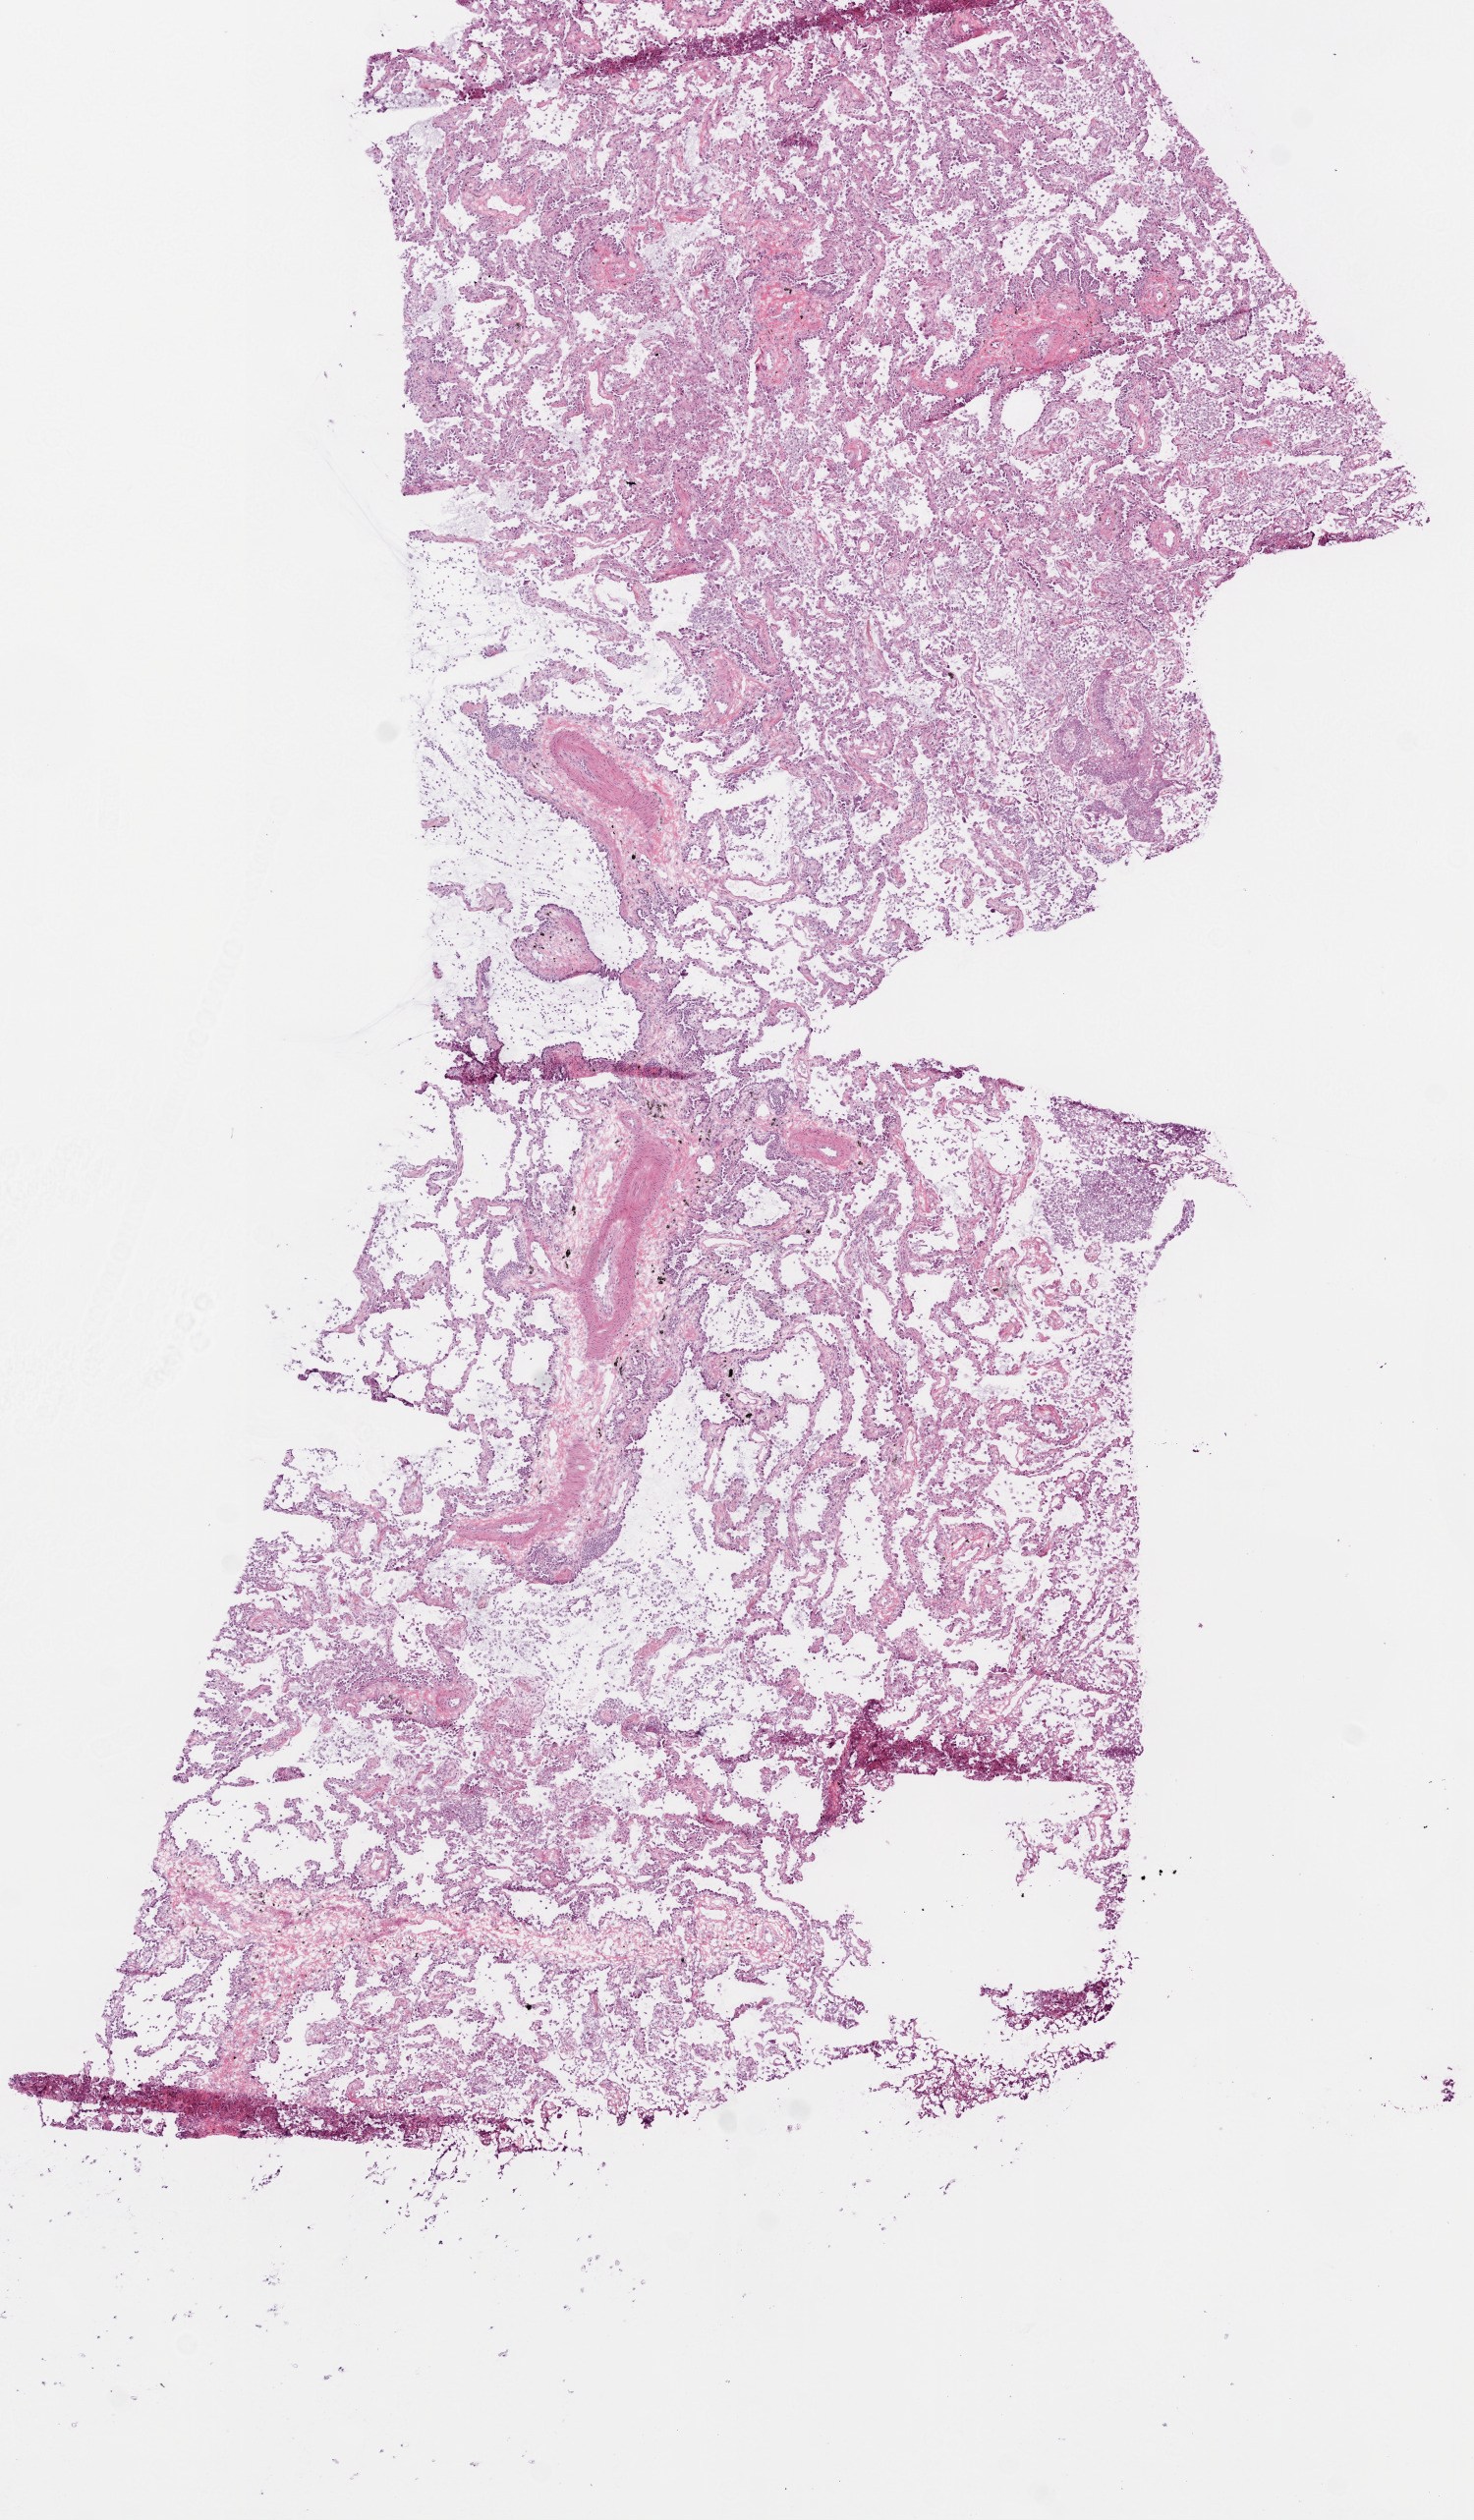
H&E whole-slide image — a low-resolution overview of the entire scanned area, about 6.0 x 10.3 mm (slide scanned at 20x); frozen section from the bottom of the tissue portion; lung, primary tumour sample. Female, age 57 years at initial diagnosis. Composition of this section per pathologist review: tumour cells 95%, tumour nuclei 75%, normal cells 0%, stromal cells 5%, necrosis 0%.
- laterality: left
- pathologic diagnosis: Adenocarcinoma, NOS (upper lobe, lung)